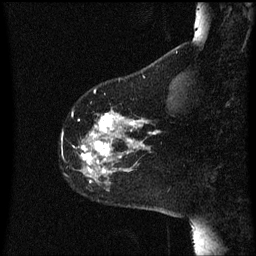
Breast MRI (dynamic contrast-enhanced), one sagittal slice; dynamic contrast-enhanced series, image 2 of 3 at this slice position (ordered by acquisition); 1.5 T; TE 4.2 ms, TR 8 ms; 256 × 256 image matrix, field of view 200 × 200 mm. Patient: female, 60 years.
Outlined on this slice (semi-automatically segmented with operator editing):
- analysis volume of interest (the breast-tissue region the enhancement analysis was run in; not a lesion): box from (x=74, y=110) to (x=158, y=191) px
- tumour enhancement mask (voxels above the 70 % enhancement threshold inside the analysis volume of interest): (x=74, y=110)–(x=158, y=183)